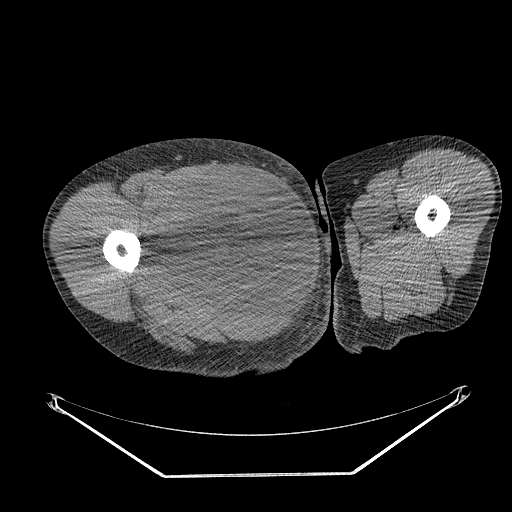
CT of an extremity soft-tissue mass (from a PET/CT study), one axial slice; position 264 of 311 along the scan axis; reconstruction kernel STANDARD; 140 kVp; soft-tissue window (W 400 / L 40 HU); 512 × 512 image matrix. Male patient. From the clinical record (not read from this slice): histological type: undifferentiated - pleiomorphic; grade: high; site of the primary tumour: right thigh.
Annotated regions visible in this slice (expert contour drawn on MRI and transferred to this co-registered scan by the dataset authors):
- gross tumour volume including surrounding oedema: bounding box (x1, y1, x2, y2) in pixels: (151, 167, 268, 280)
- gross tumour volume (mass): (157, 169, 268, 279)